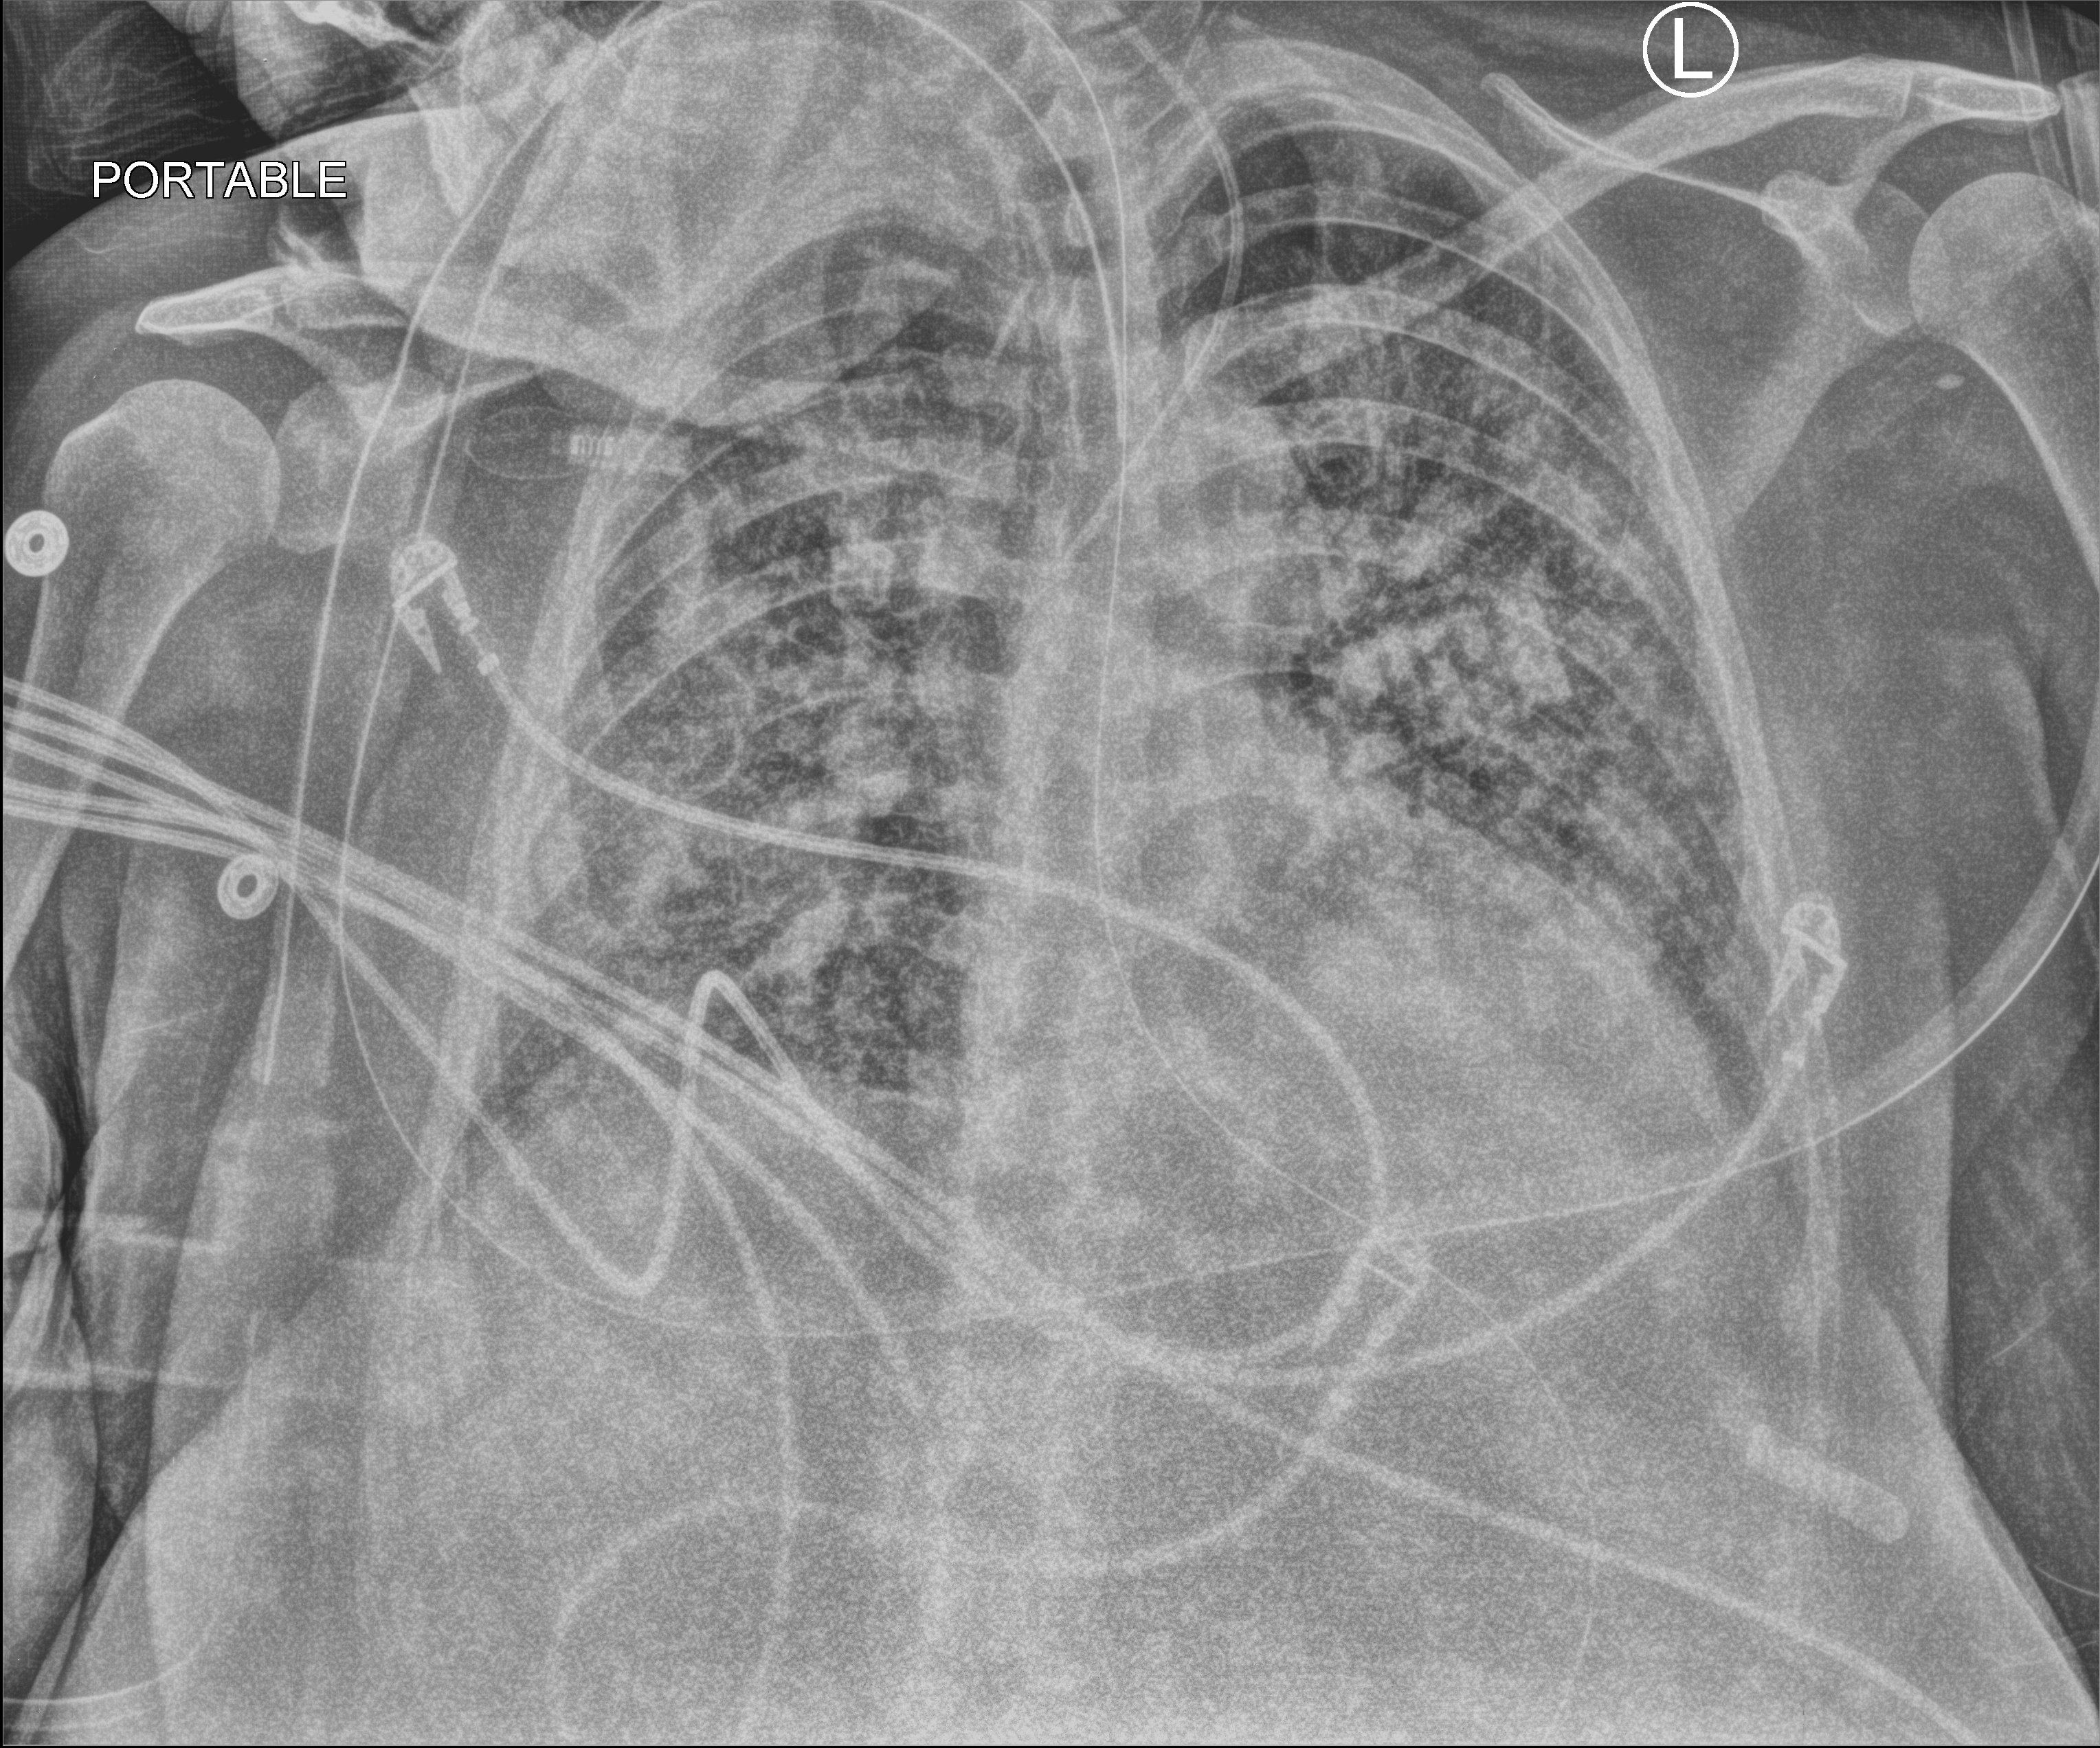
Portable chest radiograph; anteroposterior (AP) projection. Female patient hospitalised with COVID-19, age 18–59 years.
Admission-level facts for this patient (not findings on this image; timing relative to this image not recorded): mechanically ventilated during this hospital stay: yes.